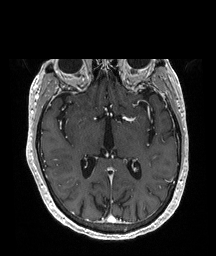
Brain MRI from a brain-tumour surgery series, one axial slice. Position 113 of 208 along the scan axis. T1-weighted post-contrast. 1 mm slice thickness. 216 × 256 image matrix, field of view 216 × 256 mm. From the clinical record (not read from this slice): histopathology: Glioblastoma; WHO grade: 4; IDH mutation: no; tumour location: Right Temporal.
Structures marked on this image (outlined manually by an expert reader):
- tumour: bounding box <60,180,76,190> (left, top, right, bottom; pixels)